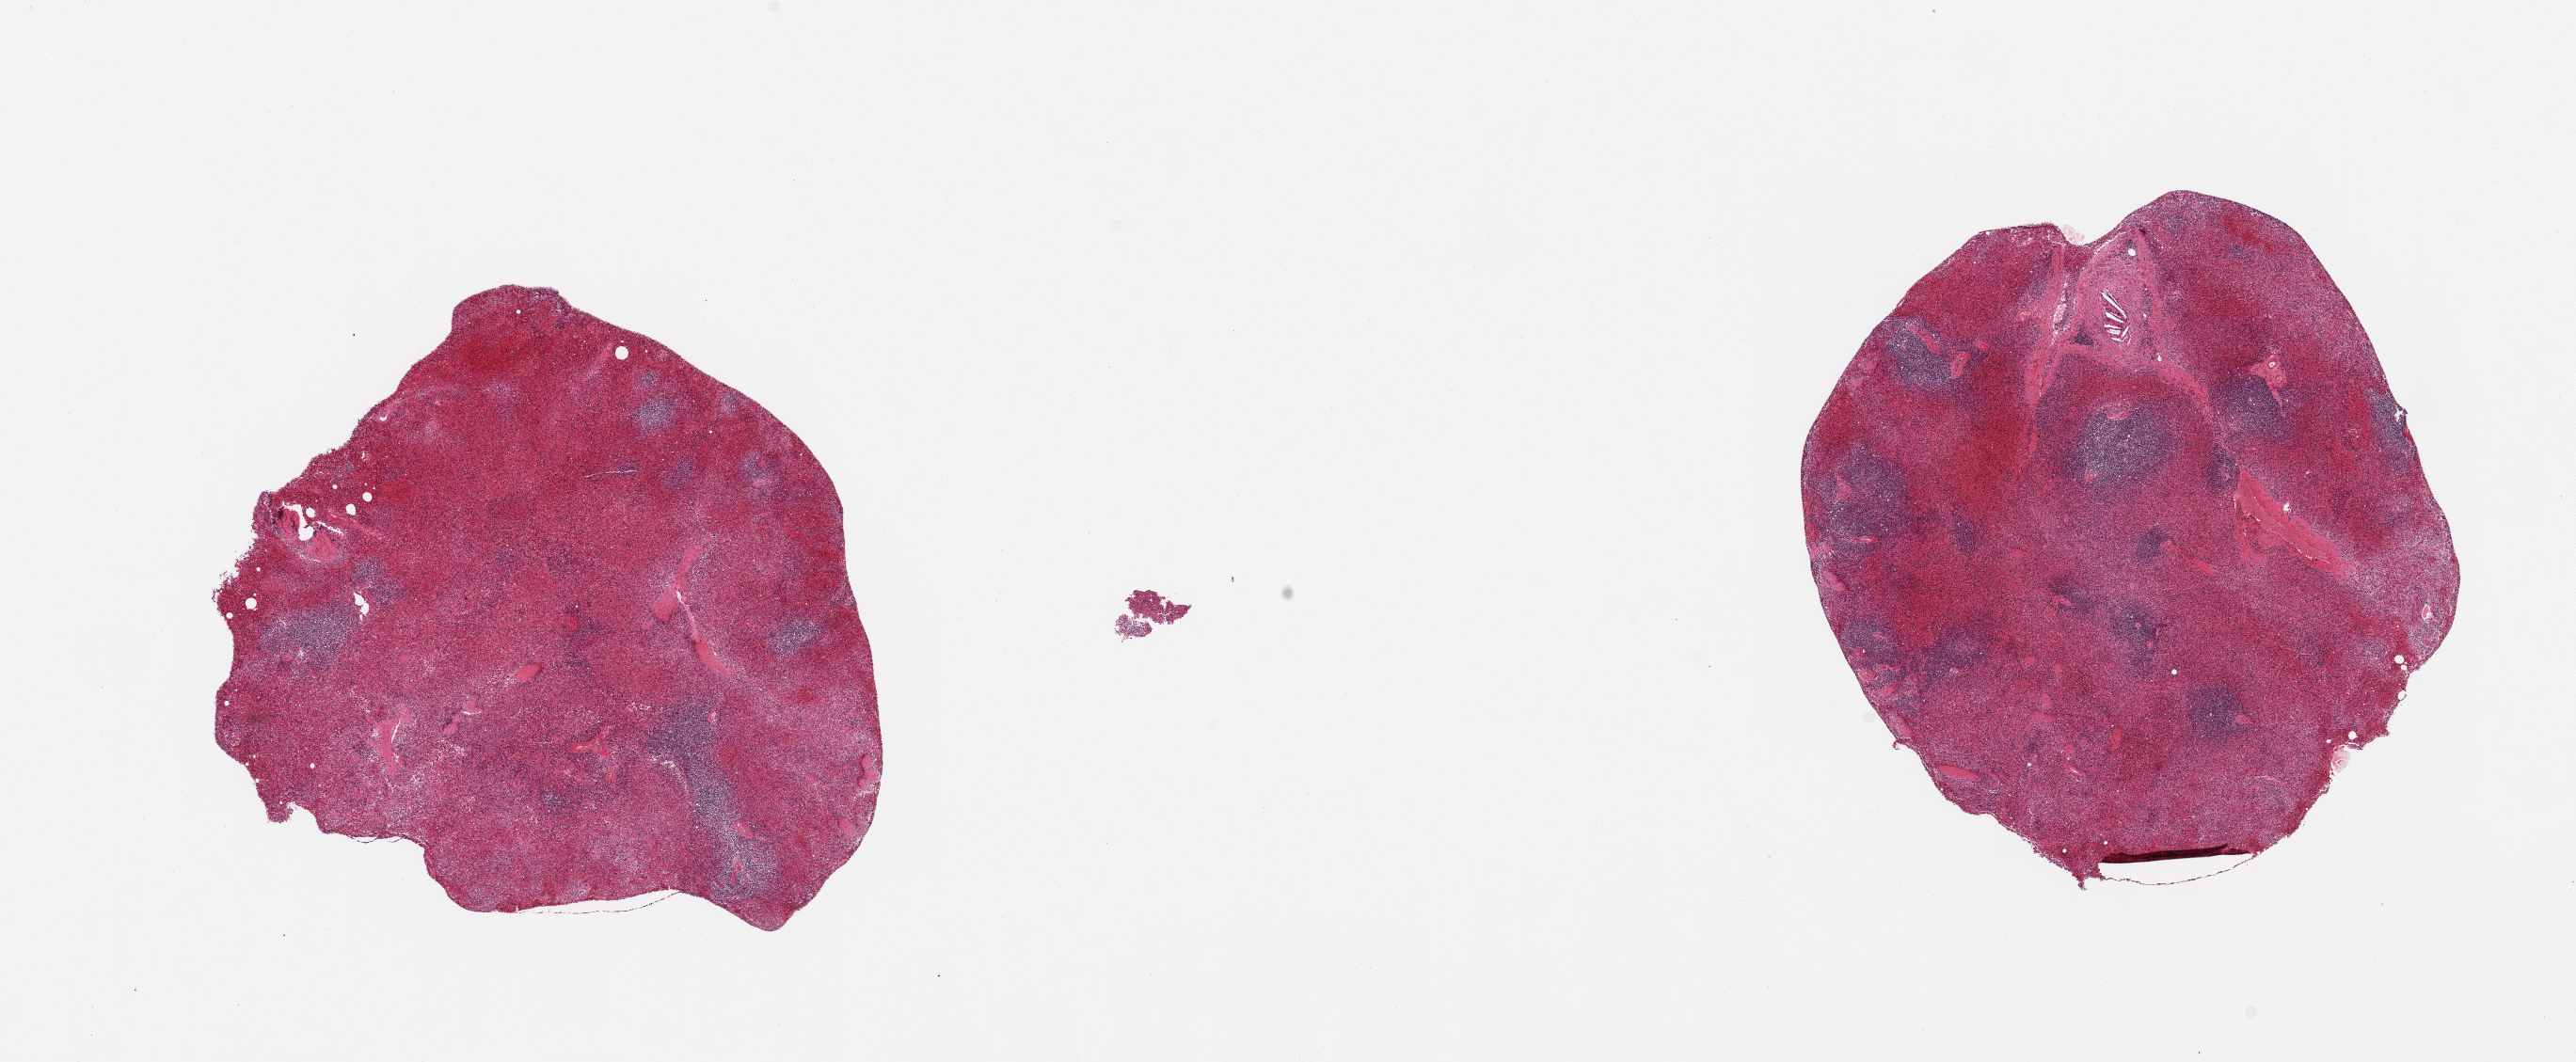
Hematoxylin and eosin (H&E) whole-slide image, low-resolution overview of the scanned area, about 21.7 x 8.9 mm; PAXgene-fixed, paraffin-embedded tissue; section of spleen (target tissue); tissue donor sample. Donor sex: male.
Review note (as recorded): 2 pieces, moderate congestion.